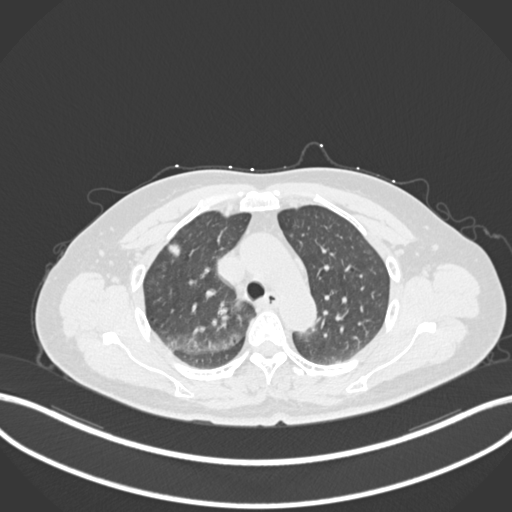
Chest CT, one axial slice. Position 166 of 223 along the scan axis. Lung window (W 1500 / L -600 HU). 1 mm slice thickness. 512 × 512 image matrix, field of view 400 × 400 mm. Patient: female, 56 years. From the clinical record (not read from this slice): clinical TNM (as recorded): T1c N0 M0.
Annotated regions visible in this slice (bounding box drawn by a radiologist):
- lung tumour (recorded histology: adenocarcinoma): bounding box (x1, y1, x2, y2) in pixels: (166, 239, 186, 261)